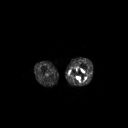
FDG PET of an extremity soft-tissue mass (from a PET/CT study), one axial slice. Slice 214 of 267 in the series (ordered by position). 3.27 mm slice thickness. 128 × 128 image matrix, field of view 700 × 700 mm. Patient: male, 44 years. From the clinical record (not read from this slice): histological type: undifferentiated pleomorphic liposarcoma; grade: high; site of the primary tumour: left thigh.
Structures marked on this image (expert contour drawn on MRI and transferred to this co-registered scan by the dataset authors):
- gross tumour volume including surrounding oedema: box from (x=69, y=66) to (x=87, y=83) px
- gross tumour volume (mass): (x=70, y=68)–(x=87, y=82)